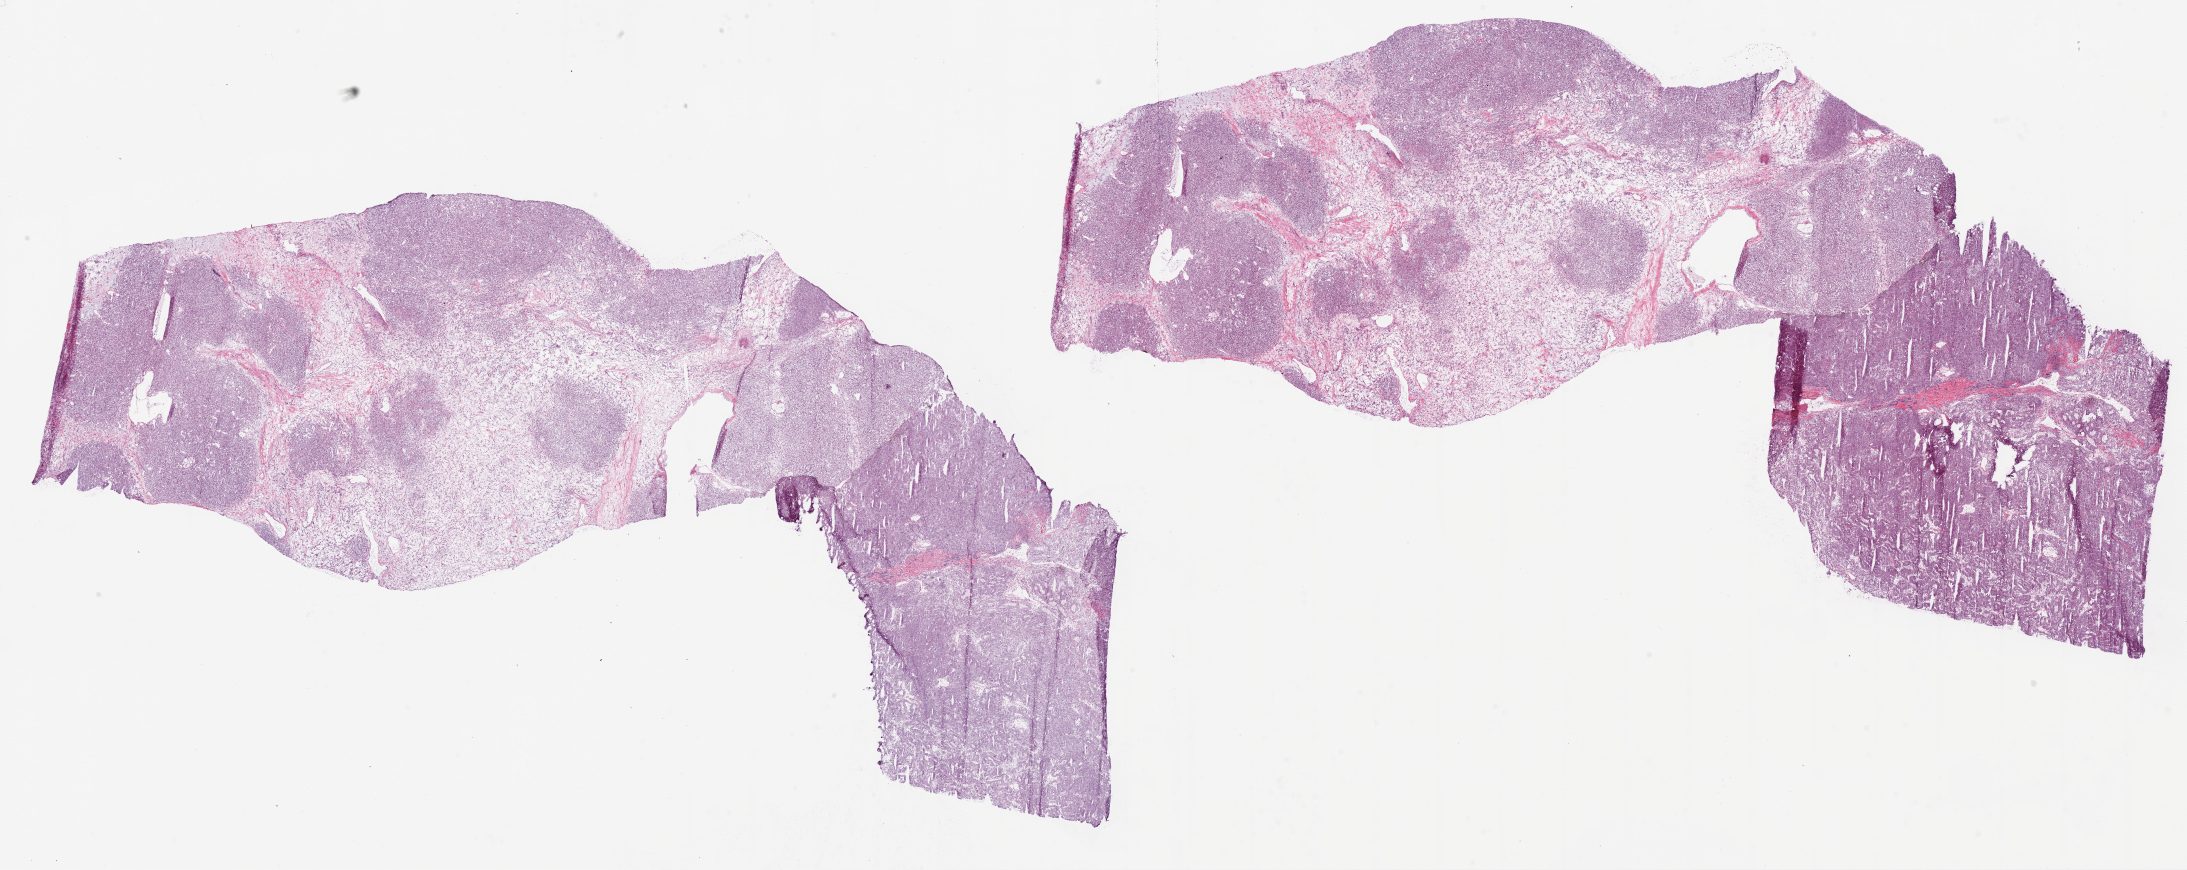
H&E-stained whole-slide image — shown as a low-resolution overview of the whole scanned area (about 35.1 x 14.0 mm, from a 20x scan), frozen section, sample: primary tumour, kidney. Patient: male, age at initial diagnosis 52 years. Histologic grade: G3 (poorly differentiated). Slide review estimates, as recorded: tumour cells 97%, tumour nuclei 78%, normal cells 0%, stromal cells 3%, necrosis 0%. Inflammatory infiltration, as recorded: lymphocyte infiltration 19%.
TNM: T2a NX M0. Diagnosis: Clear cell adenocarcinoma, NOS. Laterality: left. AJCC pathologic stage: II.